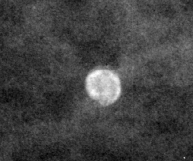
Region of interest cut from a scanned film mammogram (one marked finding), right breast, CC view, BI-RADS breast density category 3 (scale 1–4).
Finding: calcifications, morphology round and regular / eggshell; BI-RADS assessment category 2; benign; no additional work-up was recommended (benign without callback).